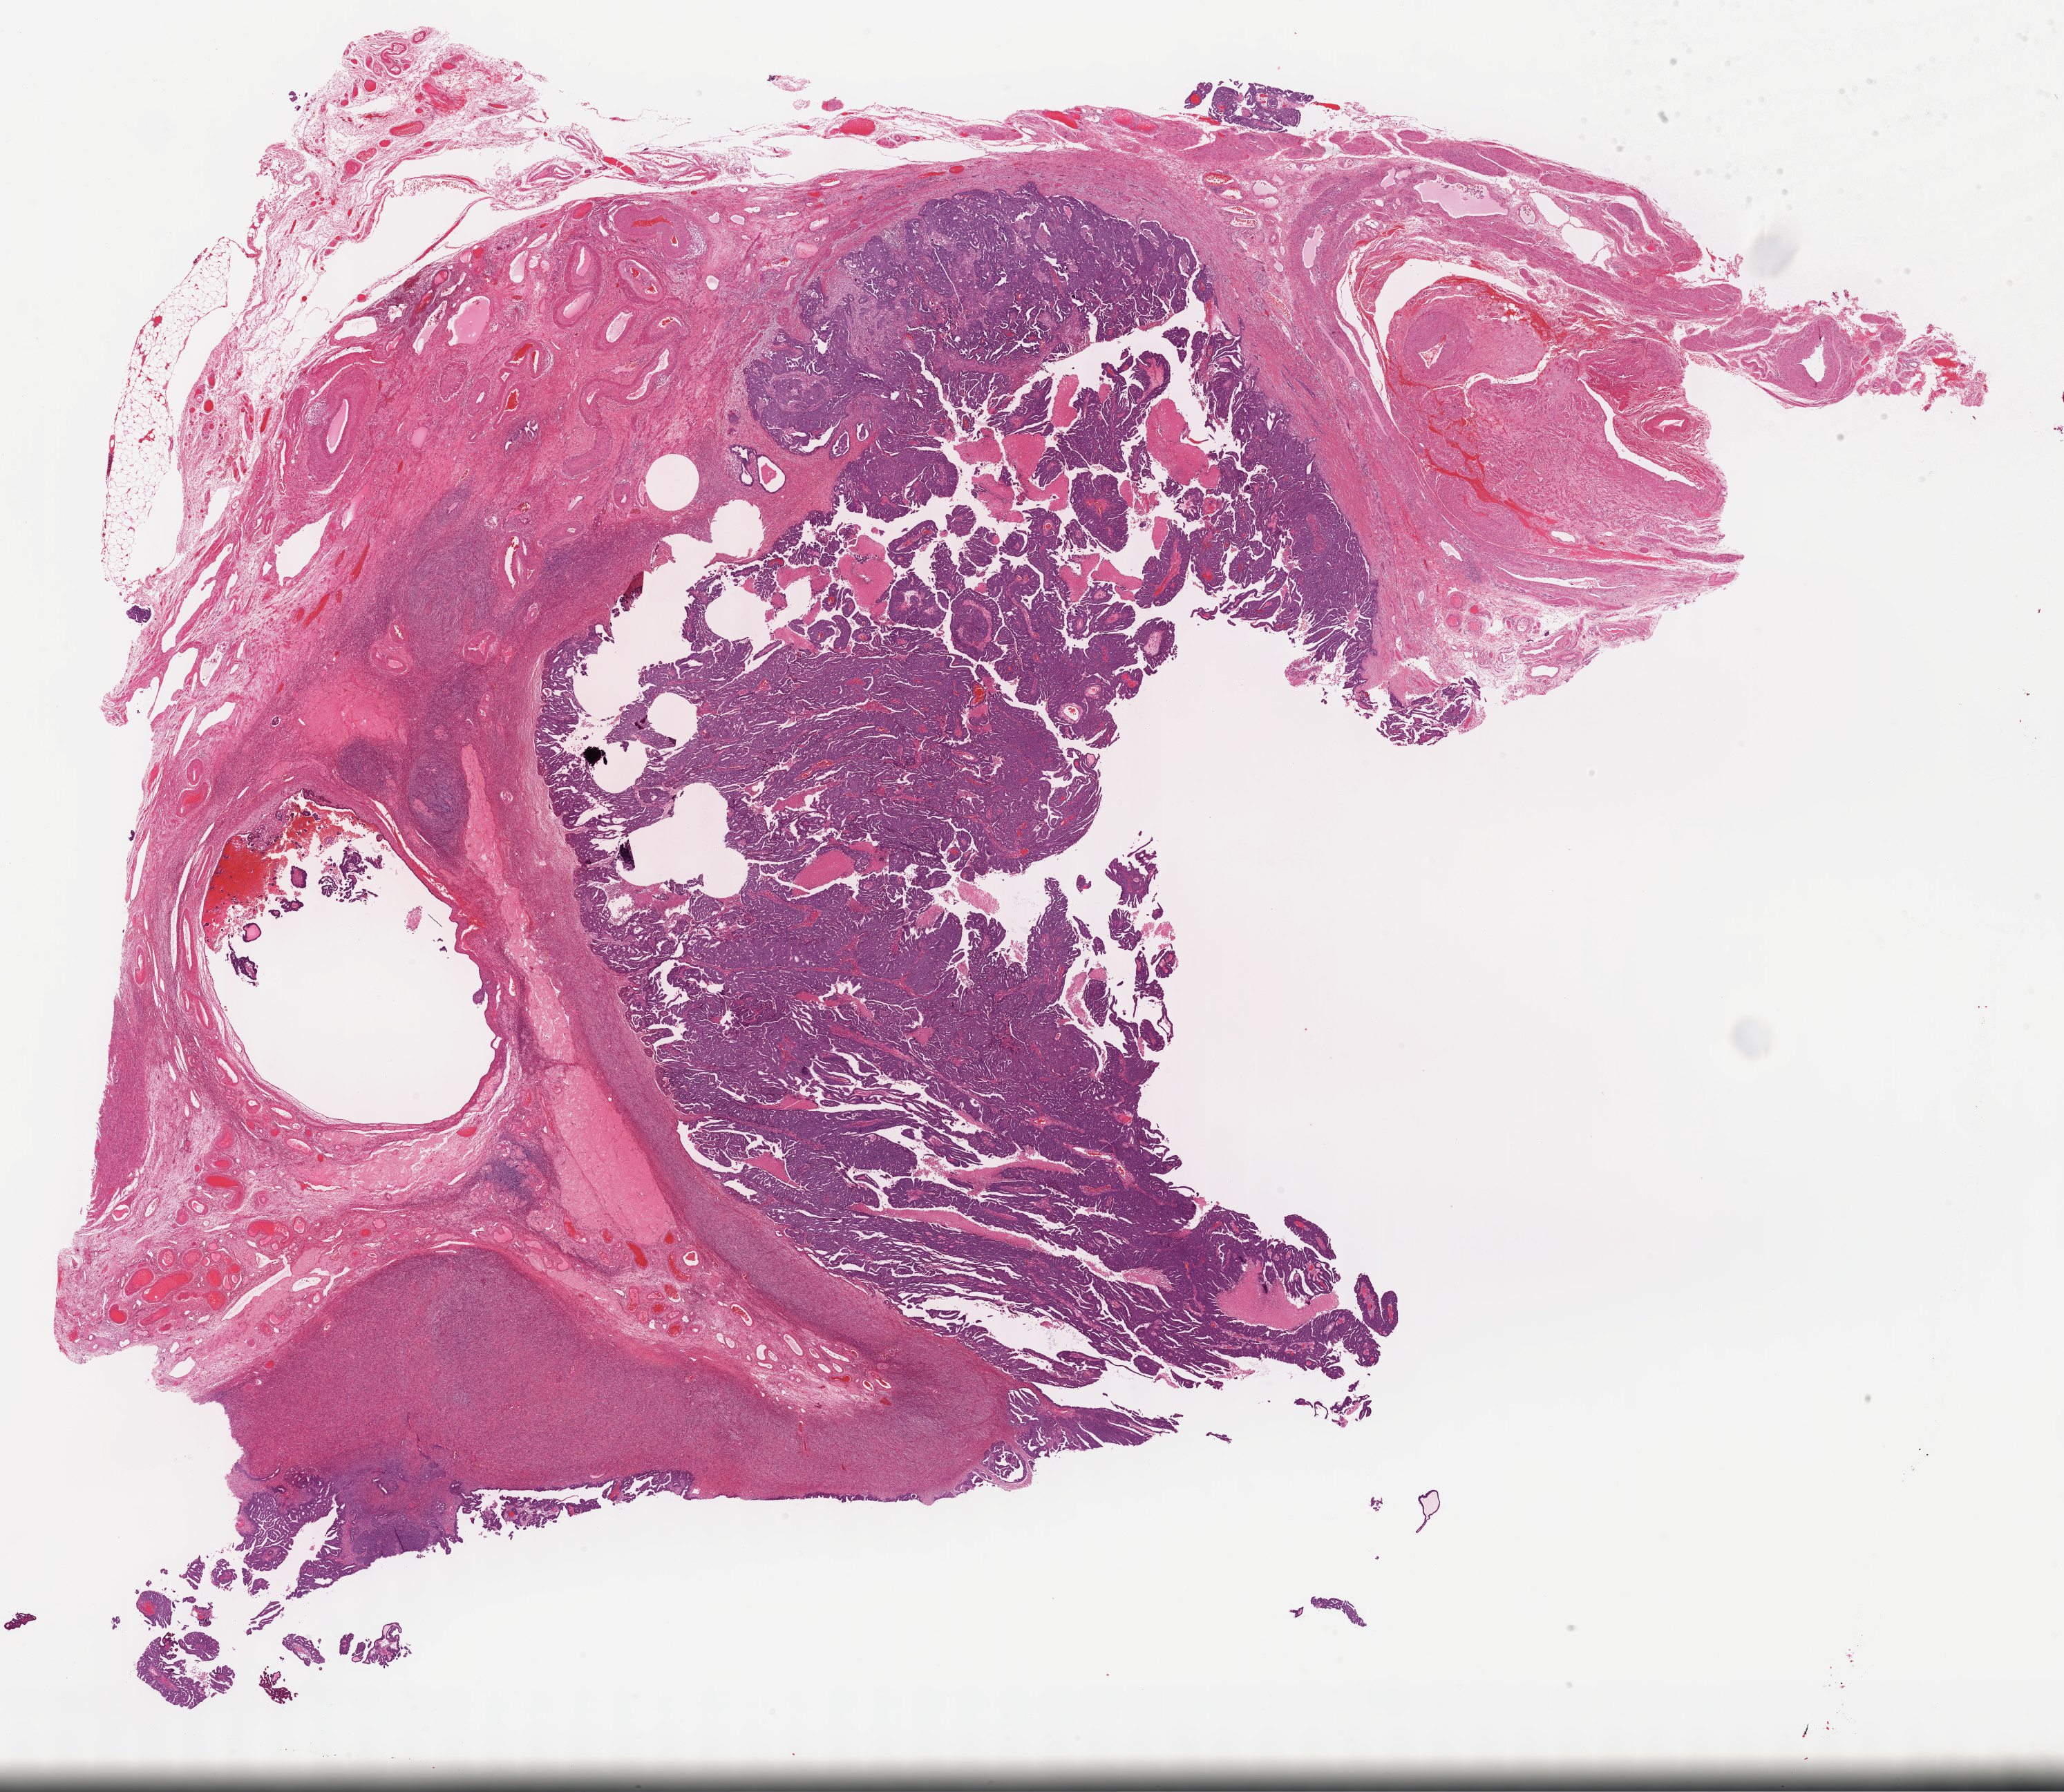
Hematoxylin and eosin (H&E) stained whole-slide image — a low-resolution overview of the entire scanned area, about 24.2 x 21.0 mm. FFPE section. Ovary, primary tumour sample. Female patient; age at initial diagnosis 67 years. Histologic grade: G3 (poorly differentiated).
- FIGO stage: IIIC
- pathologic diagnosis: Serous cystadenocarcinoma, NOS